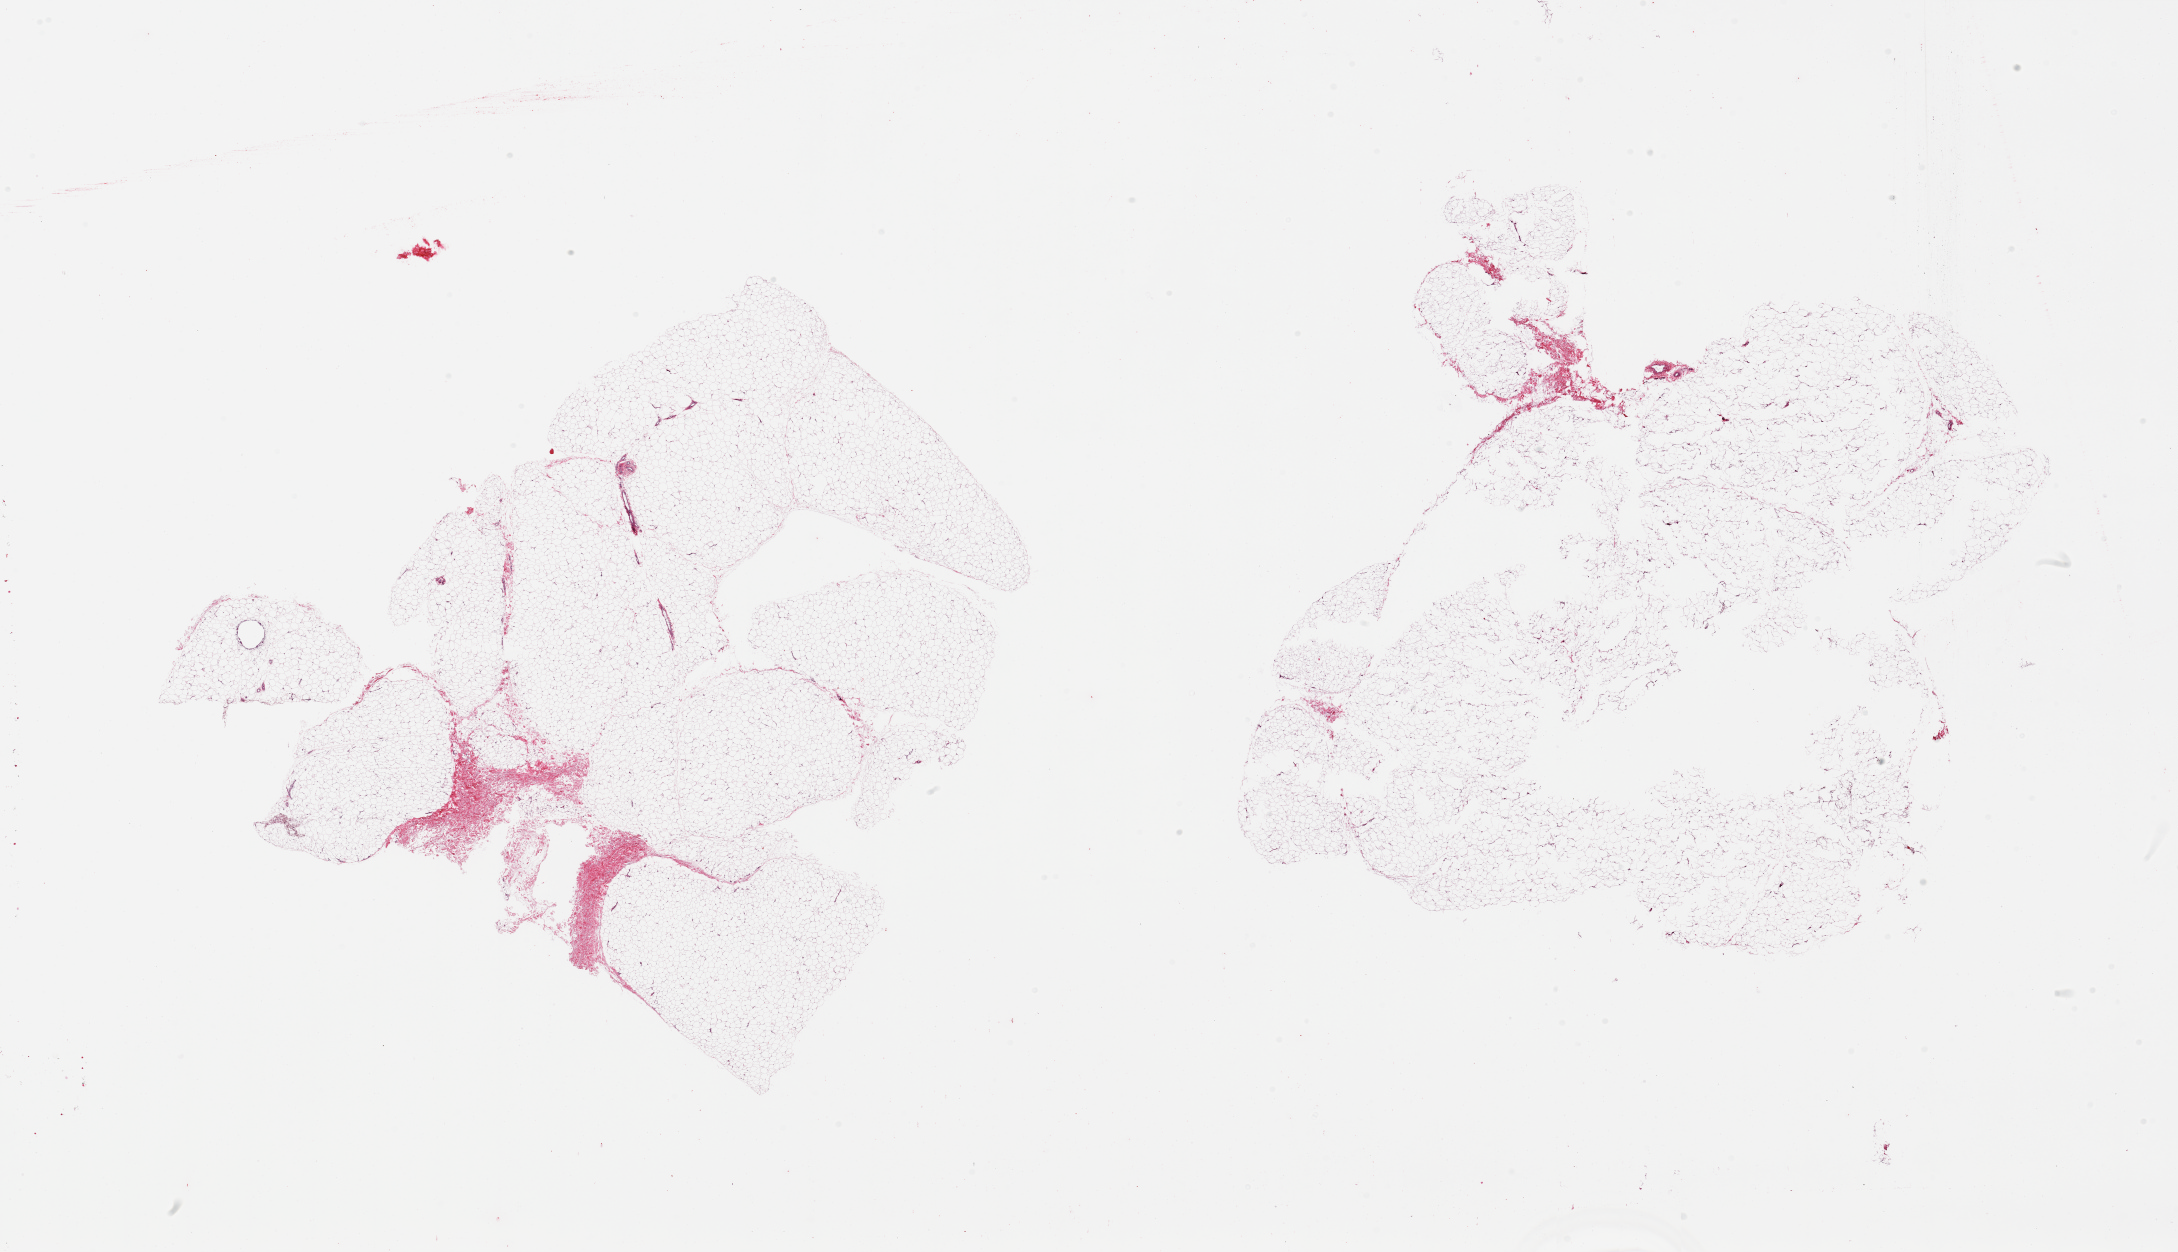
H&E whole-slide image, shown as a low-resolution overview of the whole scanned area (about 34.5 x 19.8 mm, from a 20x scan); PAXgene-fixed, paraffin-embedded tissue; sampled site (target tissue): adipose tissue; tissue donor sample. Donor sex: male.
Pathologist's review note for this sample: 2 pieces; mature fat with minimal fibrovascular component, 1 has multiple central defects (?poor fixation).